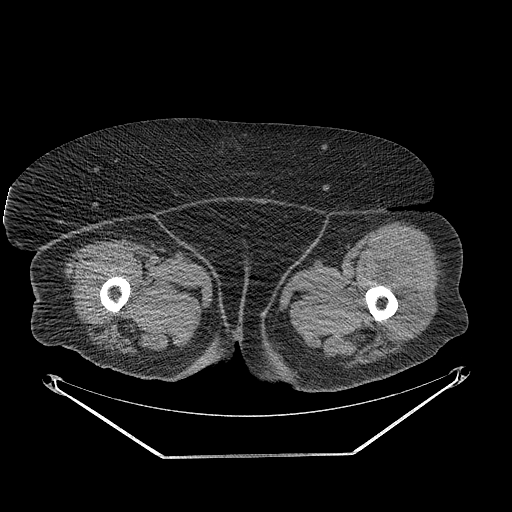
CT of an extremity soft-tissue mass (from a PET/CT study), one axial slice; slice 254 of 267 in the series (ordered by position); reconstruction kernel STANDARD; 140 kVp; soft-tissue window (W 400 / L 40 HU); 512 × 512 image matrix, field of view 500 × 500 mm. Female patient. From the clinical record (not read from this slice): histological type: undifferentiated – high grade; grade: high; site of the primary tumour: left thigh.
Structures marked on this image (expert contour drawn on MRI and transferred to this co-registered scan by the dataset authors):
- gross tumour volume including surrounding oedema: bounding box (x1, y1, x2, y2) in pixels: (379, 256, 423, 336)
- gross tumour volume (mass): (386, 256, 421, 334)